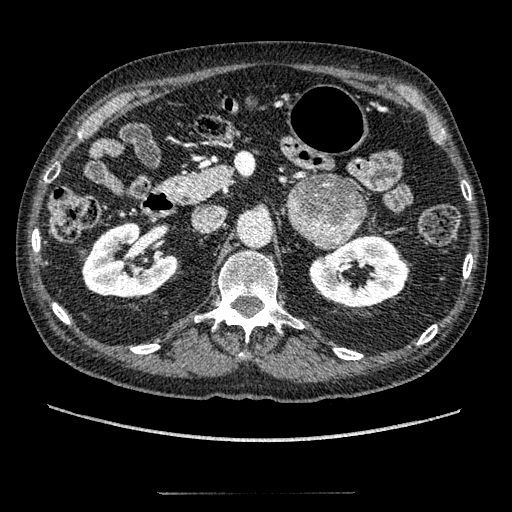
Contrast-enhanced abdominal CT, one axial slice; slice 111 of 274 in the series (ordered by position); reconstruction kernel STANDARD; intravenous contrast given; soft-tissue window (W 400 / L 40 HU); 512 × 512 image matrix. Male patient, age 69 years. Case-level facts recorded for this patient, not image findings: diagnosis: adrenocortical carcinoma; tumour side: left adrenal; tumour size at pathology: 6.1 cm; Ki-67 index: 10 %; stage (as recorded): 3.
Annotated regions visible in this slice (semi-automatic segmentation, software-assisted and operator-edited):
- mass: bounding box [x1, y1, x2, y2] px = [288, 176, 364, 249]